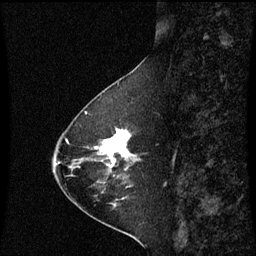
Breast MRI (dynamic contrast-enhanced), one sagittal slice. Position 22 of 60 along the scan axis. Dynamic contrast-enhanced series, image 2 of 3 at this slice position (ordered by acquisition). 1.5 T. TE 4.2 ms, TR 8.9 ms. 2 mm slice thickness. 256 × 256 image matrix, field of view 200 × 200 mm. Patient: female, 63 years. From the clinical record (not read from this slice): setting: breast cancer imaged before/during neoadjuvant chemotherapy; receptor status: HR-positive, HER2-negative.
Structures marked on this image (semi-automatically segmented with operator editing):
- analysis volume of interest (the breast-tissue region the enhancement analysis was run in; not a lesion): box from (x=96, y=126) to (x=139, y=177) px
- tumour enhancement mask (voxels above the 70 % enhancement threshold inside the analysis volume of interest): (x=97, y=130)–(x=132, y=167)